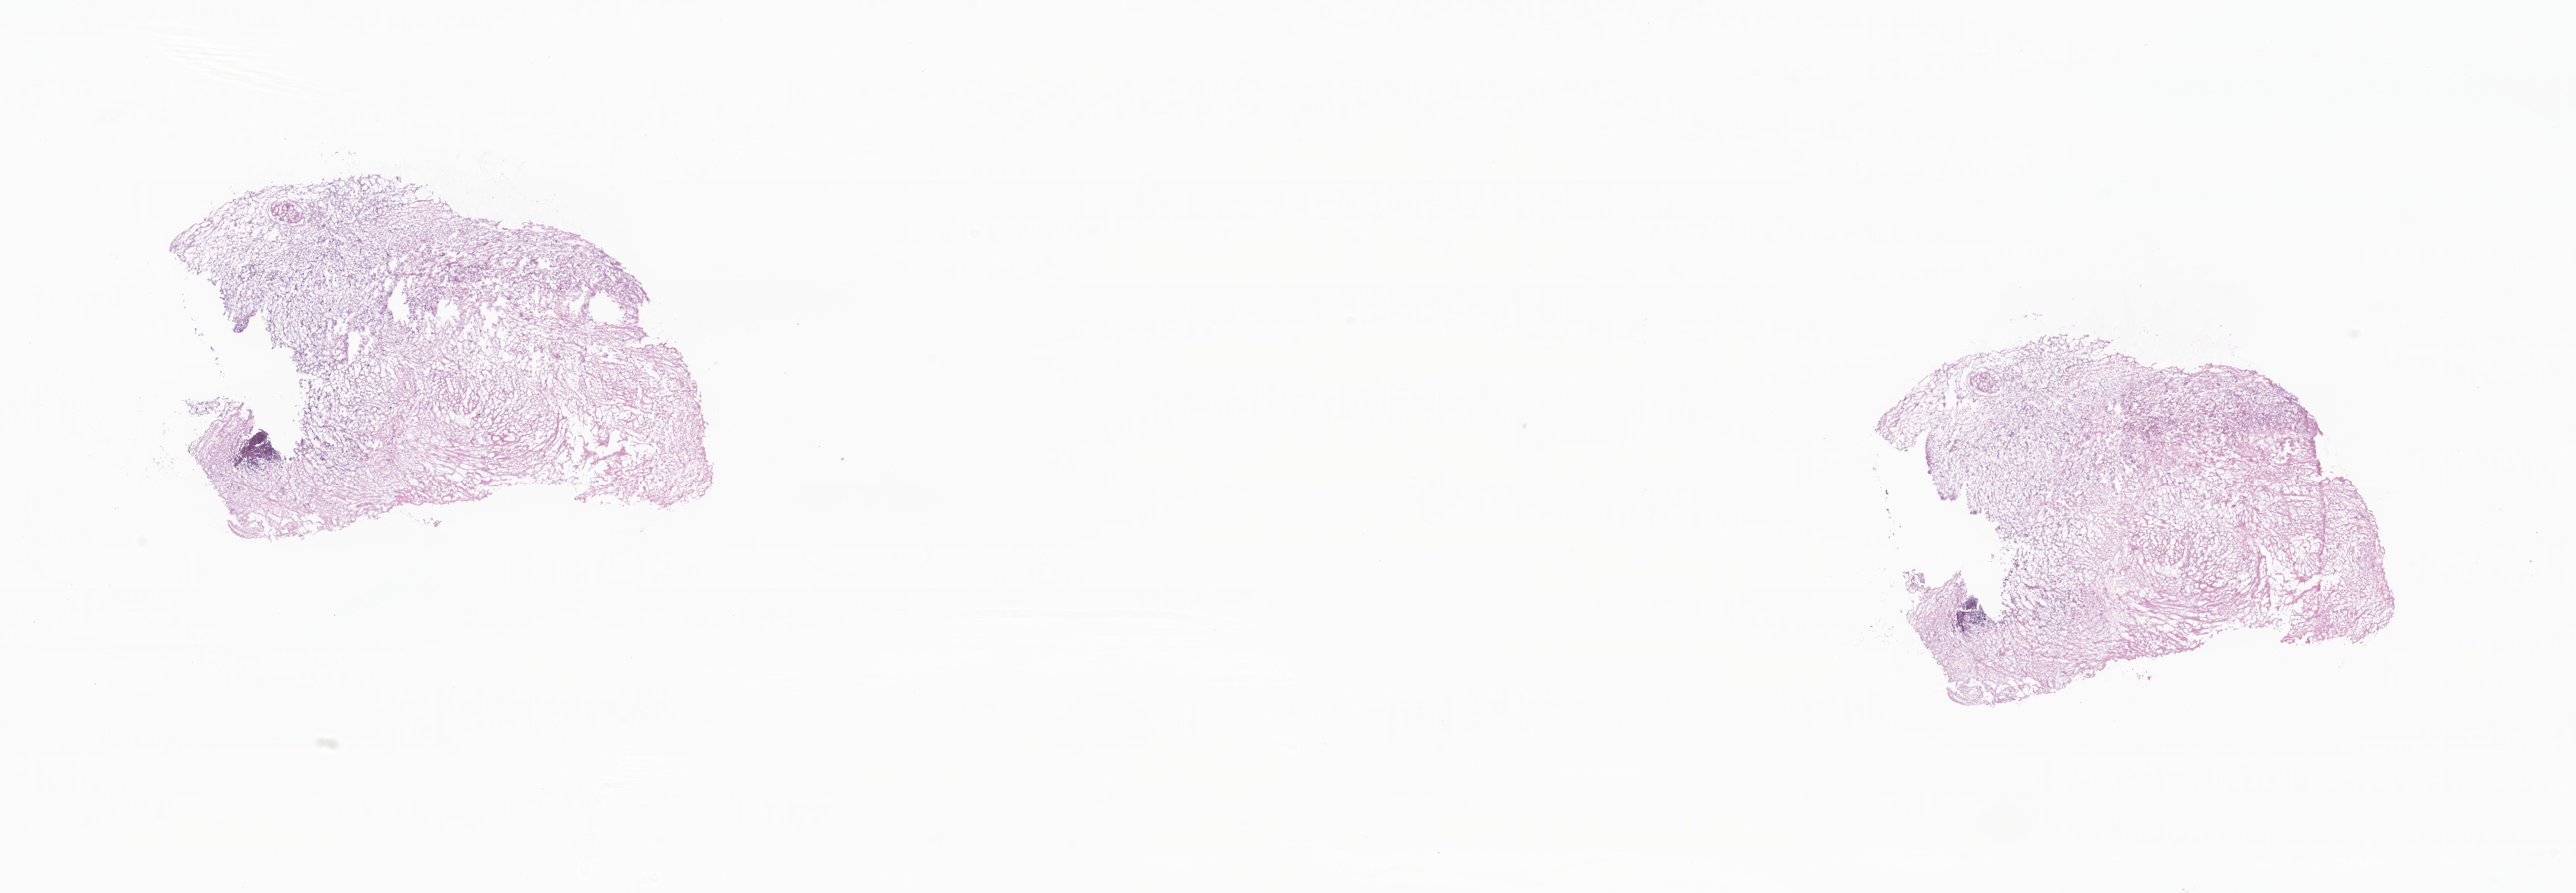
H&E whole-slide image, shown as a low-resolution overview of the whole scanned area (about 27.0 x 9.4 mm), cryosection, primary tumor, anatomic site: bladder. Male patient. Tumor grade: G3 (poorly differentiated). Slide review estimates, as recorded: tumor cells 10%, tumor nuclei 30%, stromal cells 70%, necrosis 20%, normal cells 0%. Infiltration values recorded for this section: lymphocyte infiltration 0%, monocyte infiltration 0%, neutrophil infiltration 0%.
Section: top of the tissue portion. Diagnosis: Transitional cell carcinoma, NOS.